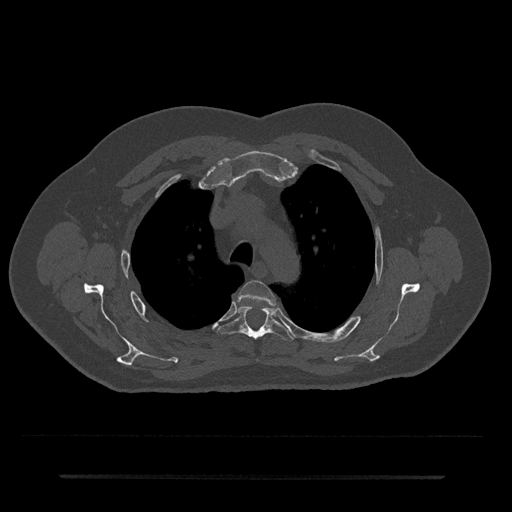
CT including the spine, one axial slice; slice 540 of 797 in the series (ordered by position); reconstruction kernel Br40s/3; bone window (W 1800 / L 400 HU); 0.5 mm slice thickness; 512 × 512 image matrix, field of view 437 × 437 mm. Patient: male, 69 years. Case-level facts recorded for this patient, not image findings: primary cancer: prostate.
Structures marked on this image (semi-automatic segmentation, software-assisted and operator-edited):
- T3 vertebra: bounding box [x1, y1, x2, y2] px = [238, 280, 276, 306]
- T4 vertebra: [218, 305, 293, 341]